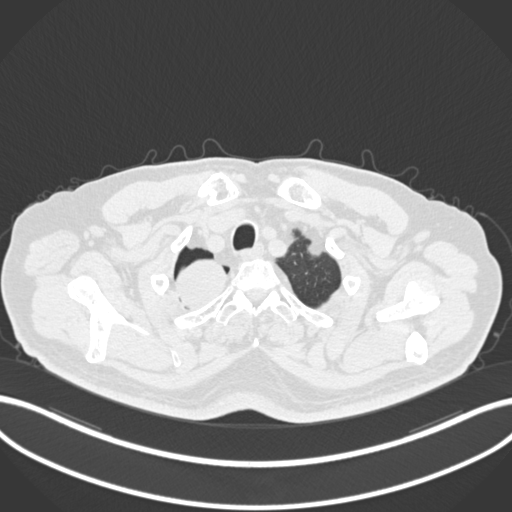
Chest CT, one axial slice. Position 196 of 218 along the scan axis. 120 kVp. Lung window (W 1500 / L -600 HU). 512 × 512 image matrix, field of view 400 × 400 mm. Patient: male, 68 years. Case-level facts recorded for this patient, not image findings: clinical TNM (as recorded): T2a N0 M0.
Annotated regions visible in this slice (rectangle marked by the reading radiologist):
- lung tumour (recorded histology: adenocarcinoma): bounding box <170,256,237,308> (left, top, right, bottom; pixels)